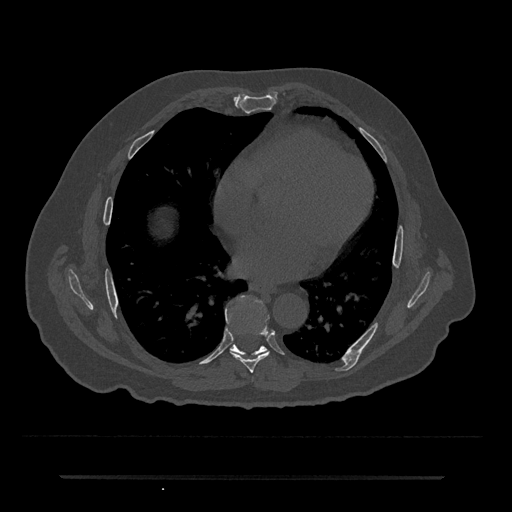
CT including the spine, one axial slice; slice 365 of 797 in the series (ordered by position); reconstruction kernel Br40s/3; 120 kVp; bone window (W 1800 / L 400 HU); 0.5 mm slice thickness; 512 × 512 image matrix, field of view 437 × 437 mm. Male patient, age 69 years. From the clinical record (not read from this slice): primary cancer: prostate.
Outlined on this slice (semi-automatically segmented with operator editing):
- T7 vertebra: bounding box [x1, y1, x2, y2] px = [226, 315, 270, 373]
- T8 vertebra: [230, 345, 267, 355]